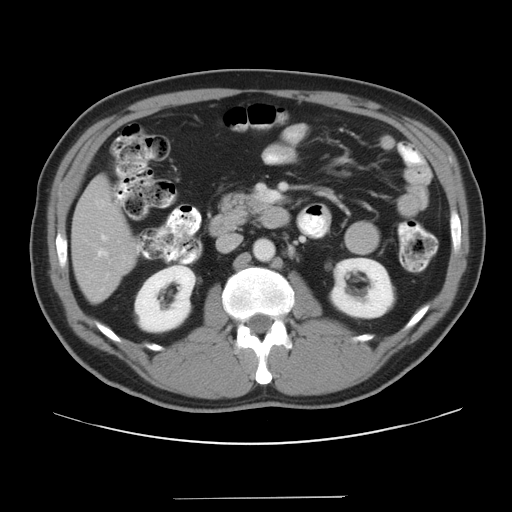
Contrast-enhanced abdominal CT, one axial slice; position 15 of 37 along the scan axis; soft-tissue window (W 400 / L 40 HU); 7.5 mm slice thickness; 512 × 512 image matrix. Male patient, age 46 years. Case-level facts recorded for this patient, not image findings: diagnosis: colorectal cancer liver metastases, imaged before liver resection; multiple liver metastases: yes; largest metastasis: 1 cm; disease in both lobes: no.
Annotated regions visible in this slice (expert manual segmentation):
- hepatic veins: bounding box (x1, y1, x2, y2) in pixels: (98, 235, 107, 256)
- liver: (73, 179, 135, 302)
- planned liver remnant (the part of the liver to remain after resection): (73, 179, 135, 302)